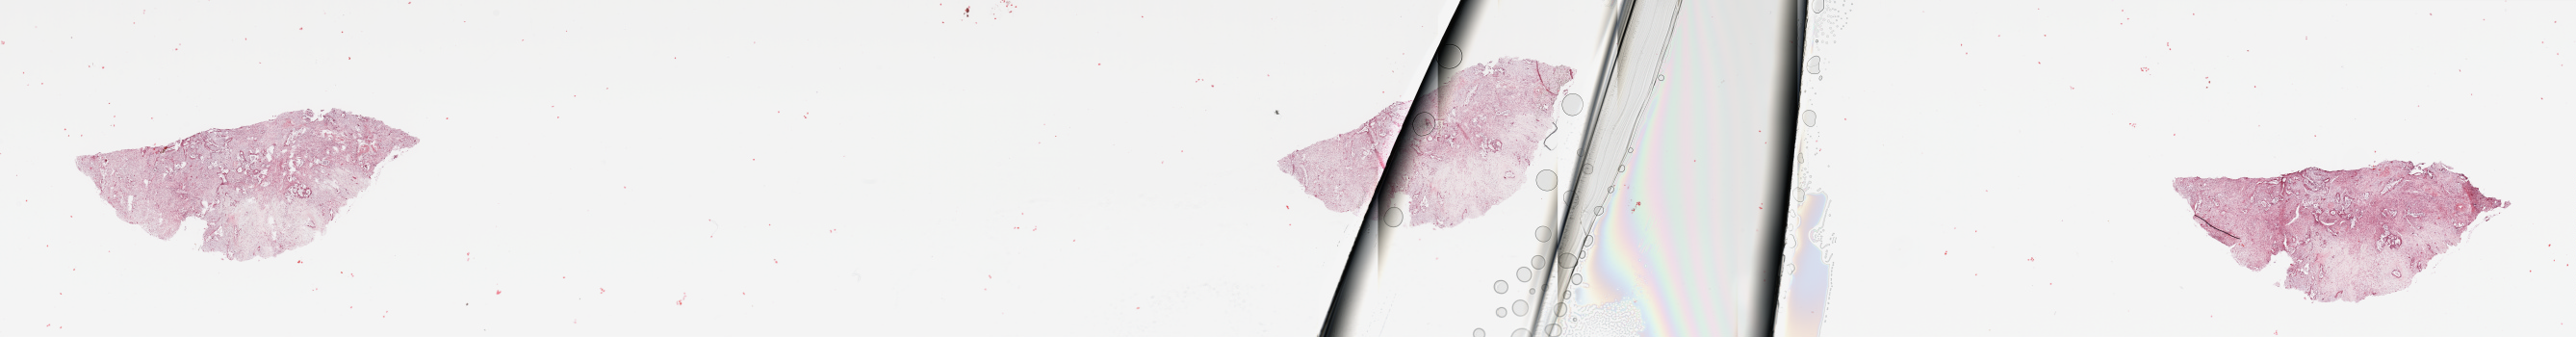
H&E whole-slide image, low-resolution overview of the scanned area, about 42.3 x 5.5 mm (slide scanned at 20x); tumour tissue sample, sampled site: pancreas. Patient: male, age 57 years. Histologic grade: G3 (poorly differentiated). Slide review estimates, as recorded: tumour nuclei 20%, necrosis 0%.
AJCC pathologic stage: IV. Primary tumour site (as recorded): head. Diagnosis: Infiltrating duct carcinoma, NOS.